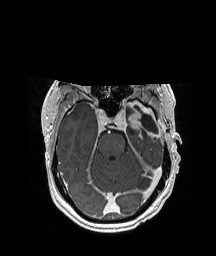
Brain MRI from a brain-tumour surgery series, one axial slice. Position 134 of 208 along the scan axis. T1-weighted post-contrast. 216 × 256 image matrix, field of view 228 × 270 mm. Case-level facts recorded for this patient, not image findings: histopathology: Glioblastoma; WHO grade: 4; IDH mutation: no; tumour location: Left Anterior/Superior Temporal.
Outlined on this slice (expert manual segmentation):
- previous resection cavity: bounding box [x1, y1, x2, y2] px = [134, 106, 158, 133]
- tumour: [132, 99, 158, 143]